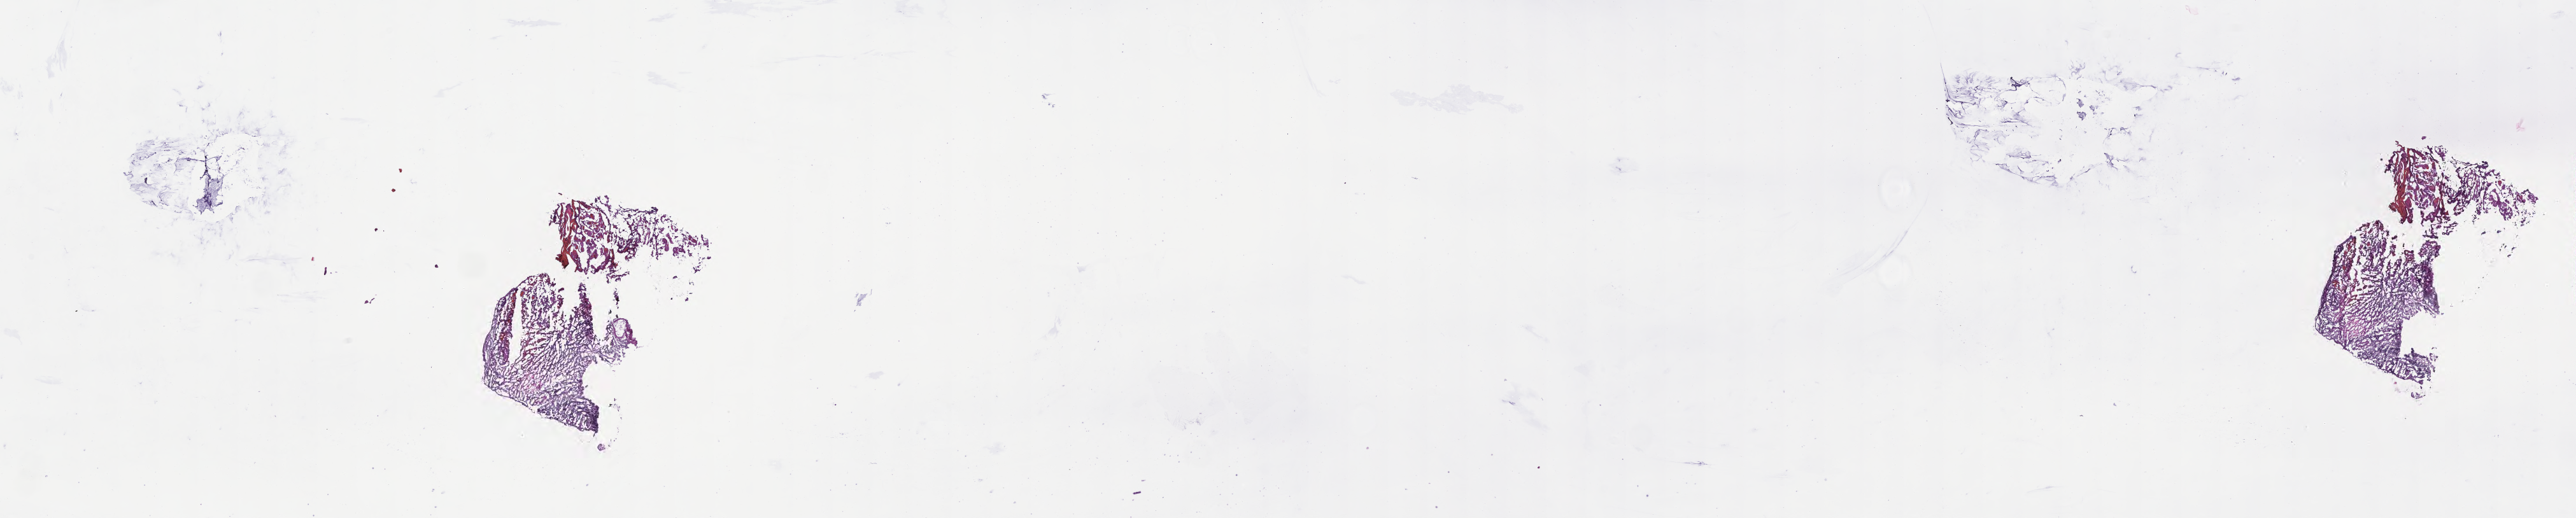
Whole-slide image, haematoxylin and eosin stain of tumor tissue from the brain — low-resolution overview of the scanned area, about 32.7 x 6.6 mm; cryosection (OCT / tissue freezing medium). Male patient, age 148 months.
Recorded diagnosis: Neoplasm, malignant.